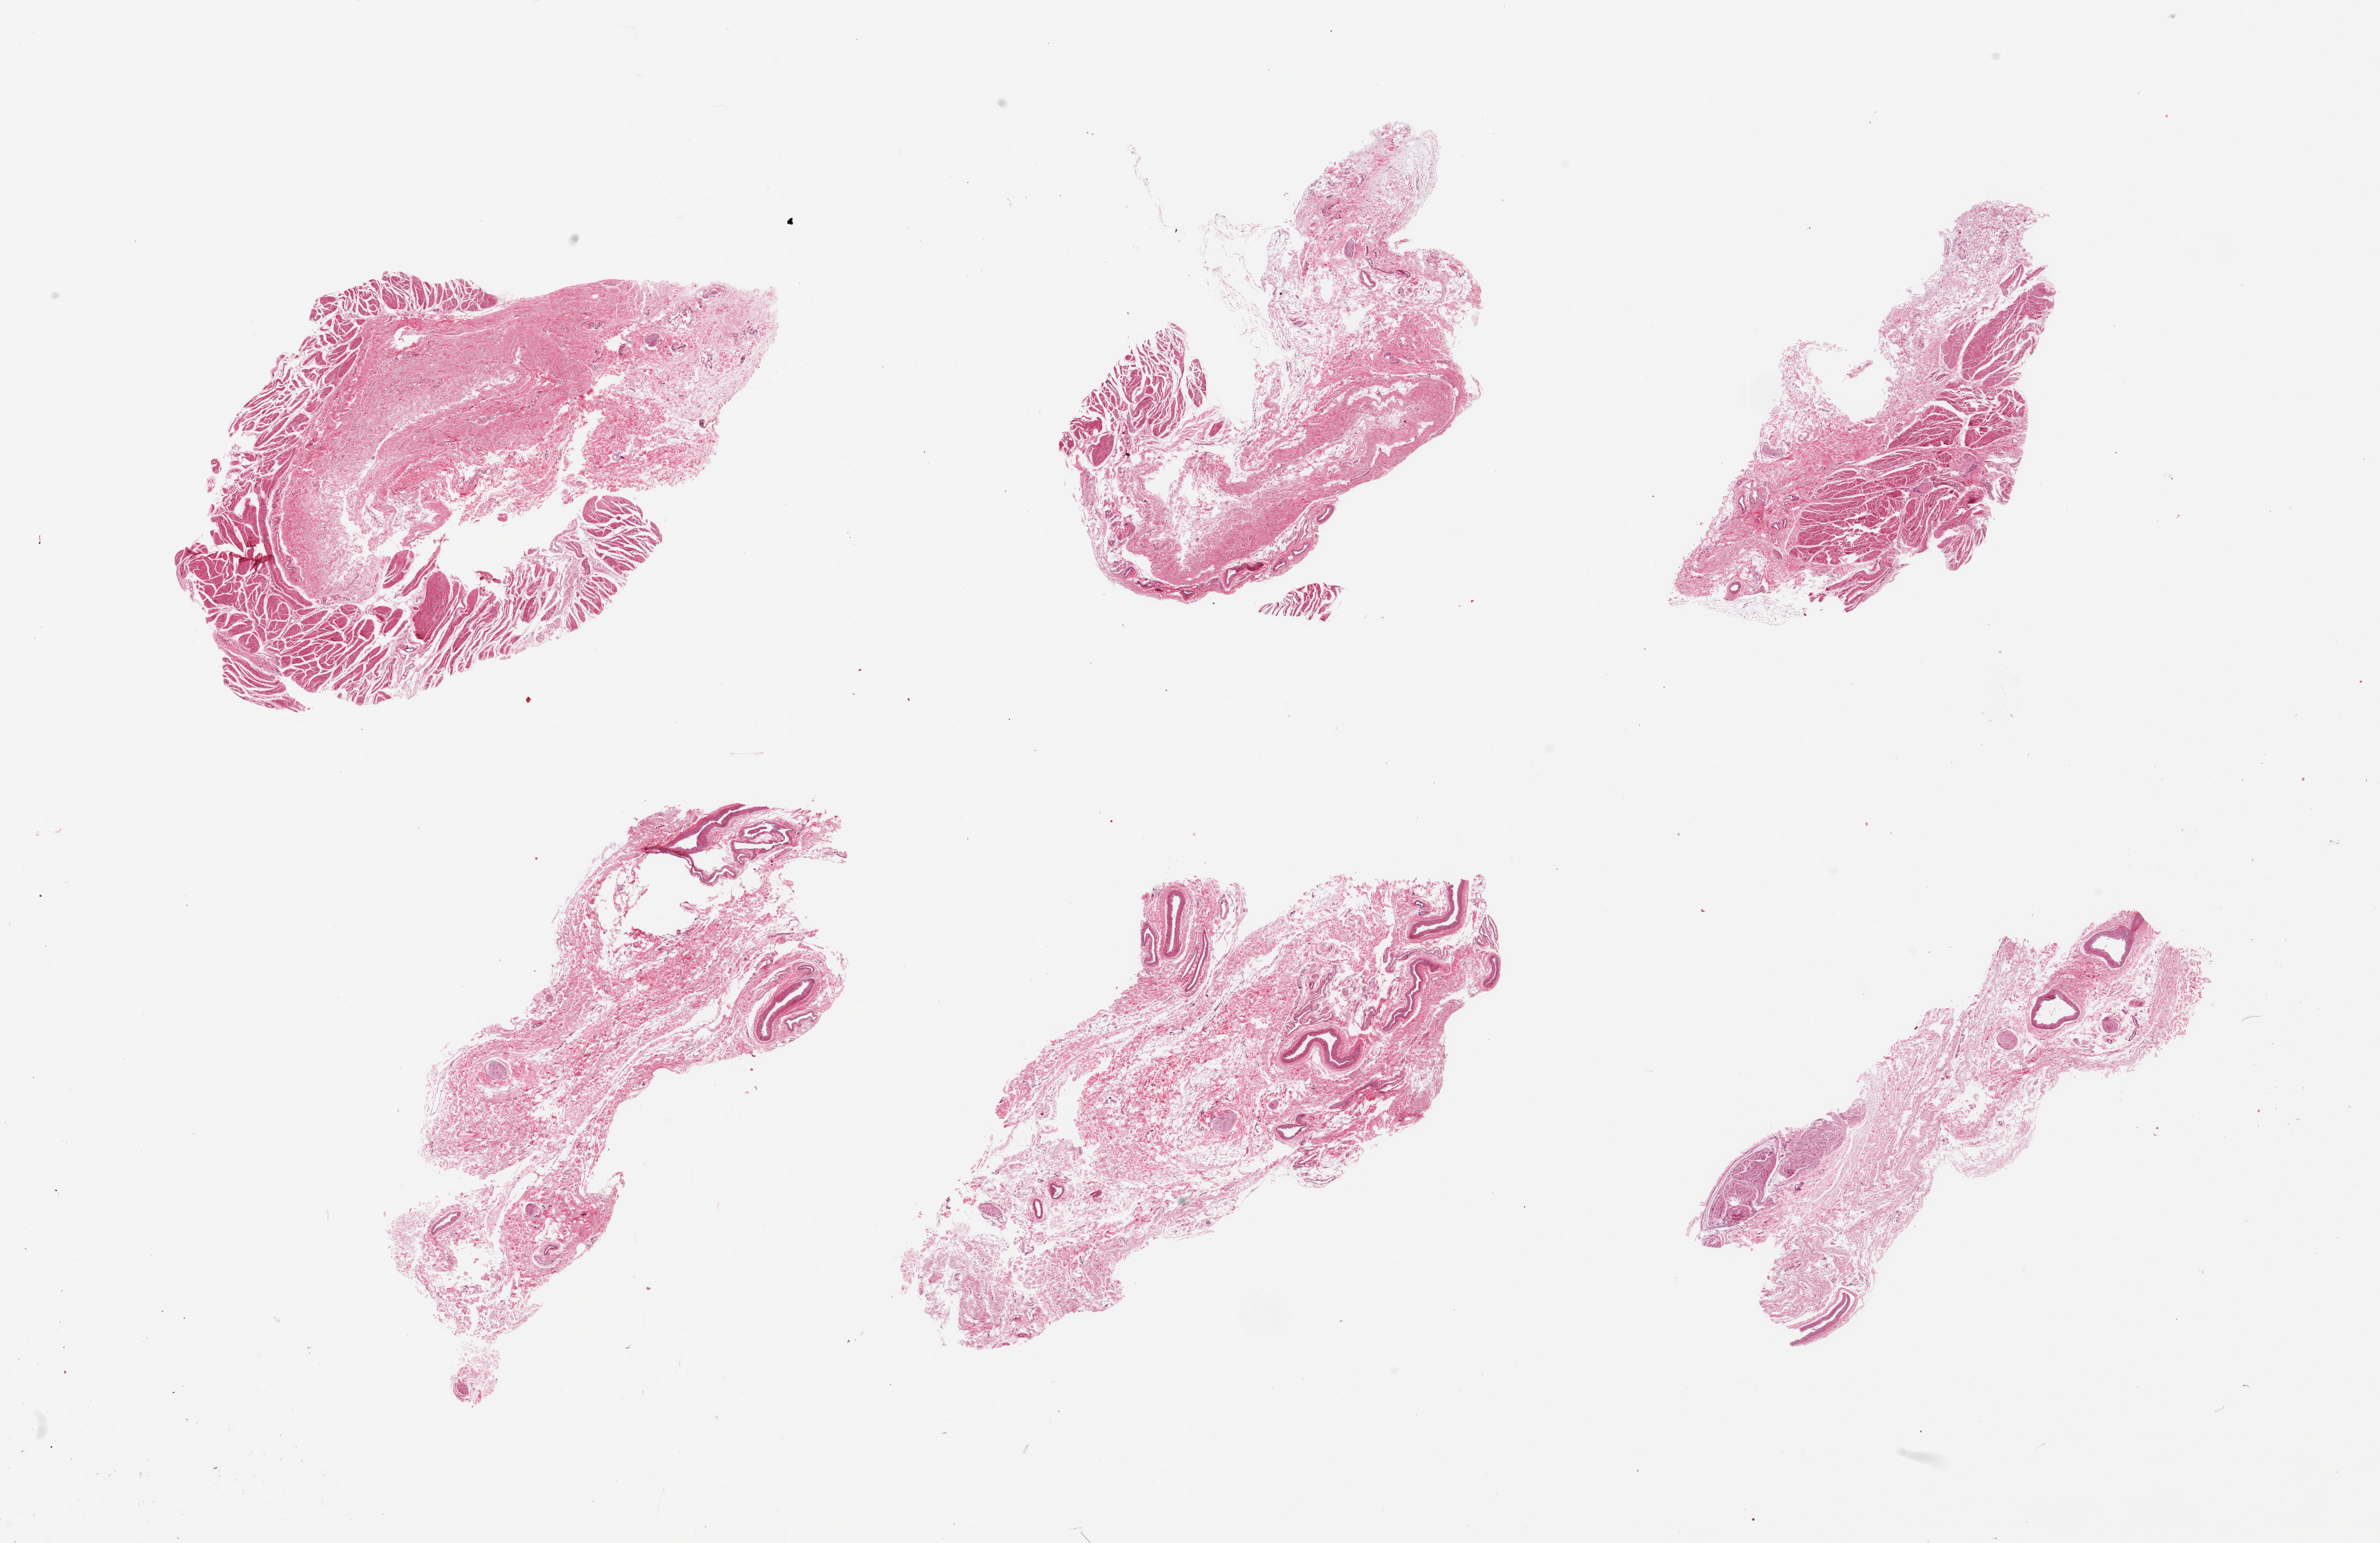
H&E whole-slide image, brightfield, shown as a low-resolution overview of the whole scanned area (about 29.5 x 19.1 mm); PAXgene-fixed paraffin-embedded (PFPE) section; section of gastroesophageal junction (target tissue); tissue donor sample. Donor sex: female.
Reviewer comment on this tissue sample: 6 pieces; minor representation of muscularis, predominantly submucosa.